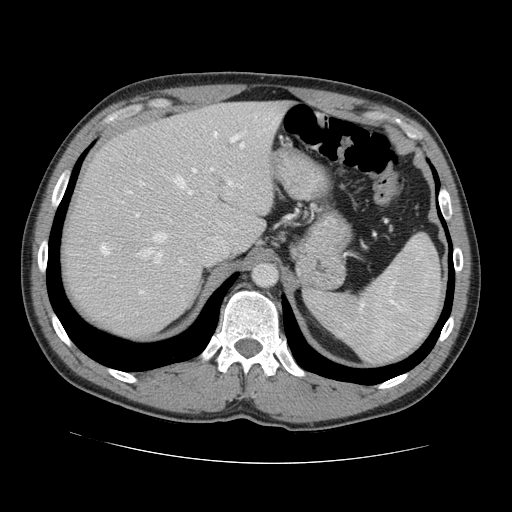
Contrast-enhanced abdominal CT, one axial slice. Slice 99 of 131 in the series (ordered by position). Intravenous contrast given. Soft-tissue window (W 400 / L 40 HU). 2.5 mm slice thickness. 512 × 512 image matrix, field of view 380 × 380 mm. Male patient, age 40 years. Case-level facts recorded for this patient, not image findings: diagnosis: colorectal cancer liver metastases, imaged before liver resection; multiple liver metastases: yes.
Annotated regions visible in this slice (outlined manually by an expert reader):
- hepatic veins: bounding box [x1, y1, x2, y2] px = [139, 136, 244, 263]
- liver: [64, 102, 285, 336]
- planned liver remnant (the part of the liver to remain after resection): [98, 102, 286, 251]
- portal vein (with intrahepatic branches): [192, 133, 244, 186]